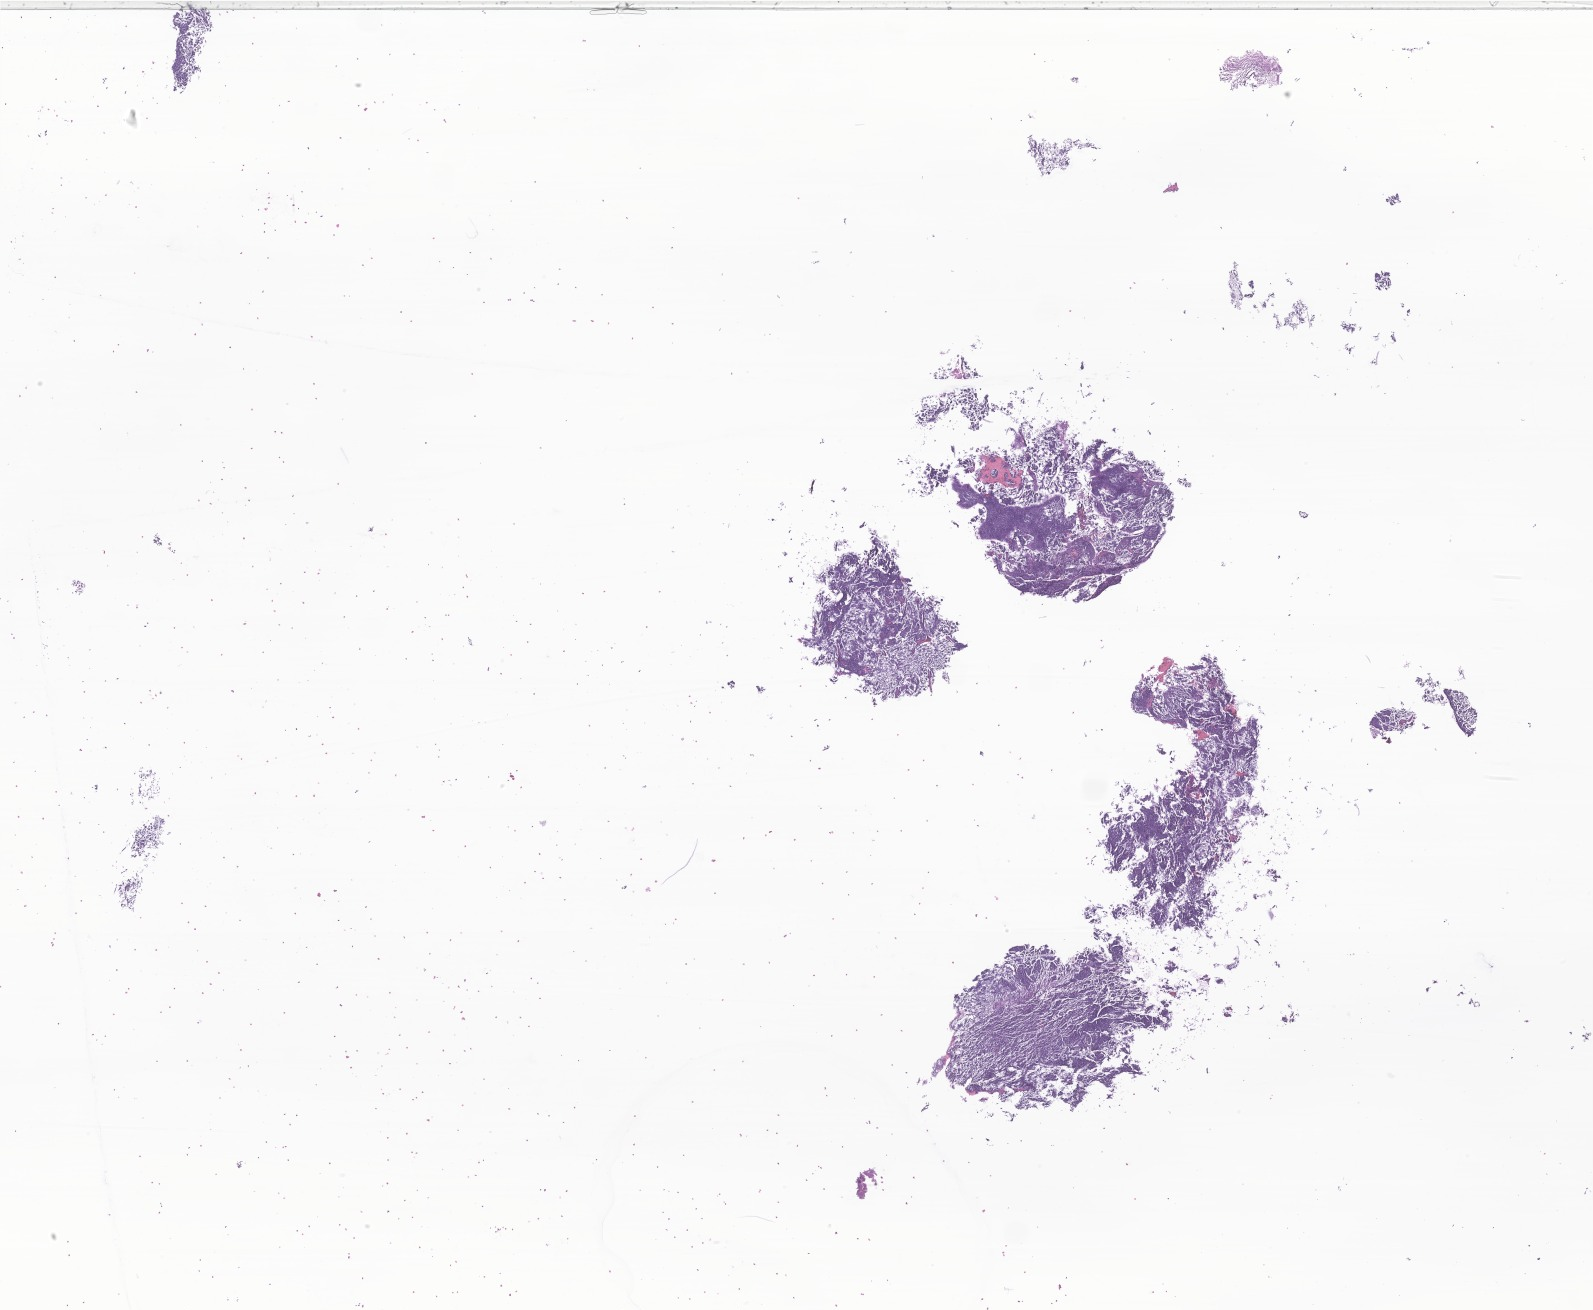
Digitized H&E-stained section of tumor tissue from the cerebellum — a low-resolution overview of the entire scanned area, about 26.9 x 22.1 mm; formalin-fixed, paraffin-embedded (FFPE) tissue. Patient: male, age 53 months (4 years 5 months).
Diagnosis (ICD-O-3 morphology term): Desmoplastic nodular medulloblastoma.